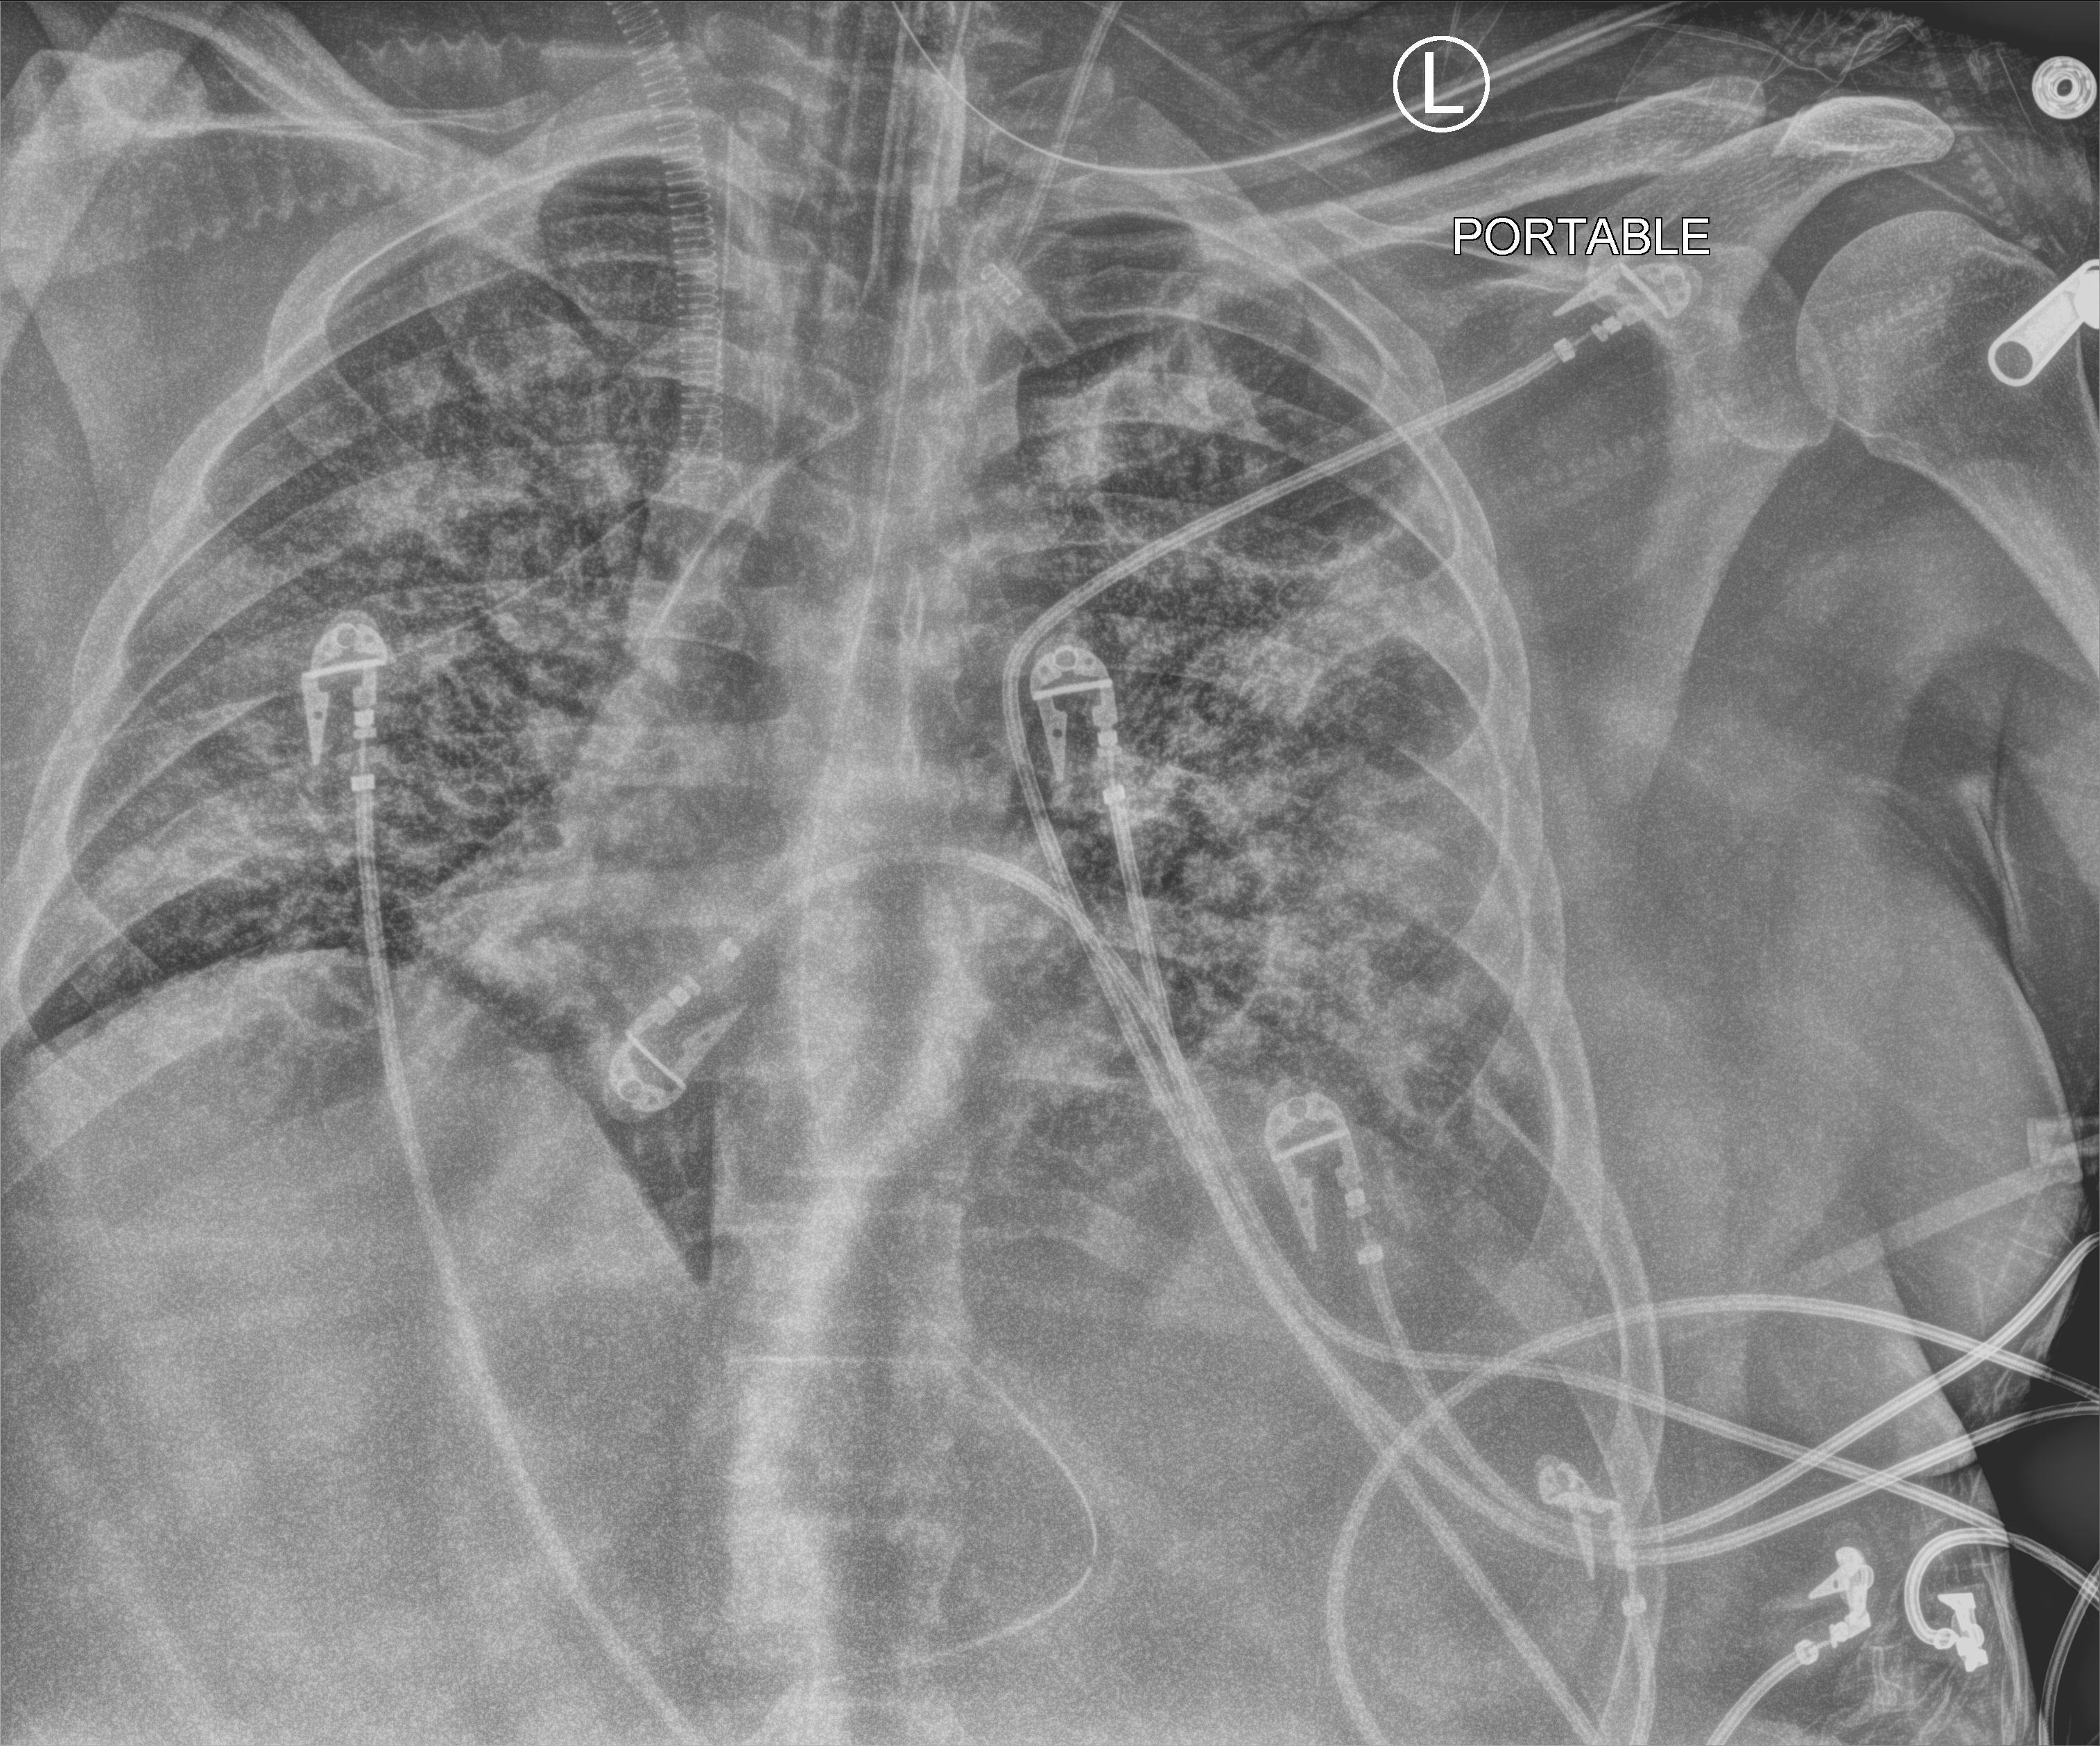
Bedside chest radiograph (computed radiography), anteroposterior (AP) projection. Patient hospitalised with COVID-19, aged 18–59 years.
From the hospital-stay record, not from the radiograph (when in the stay this image was taken is not recorded):
- admitted to intensive care during this hospital stay: yes
- smoking status (admission record): never